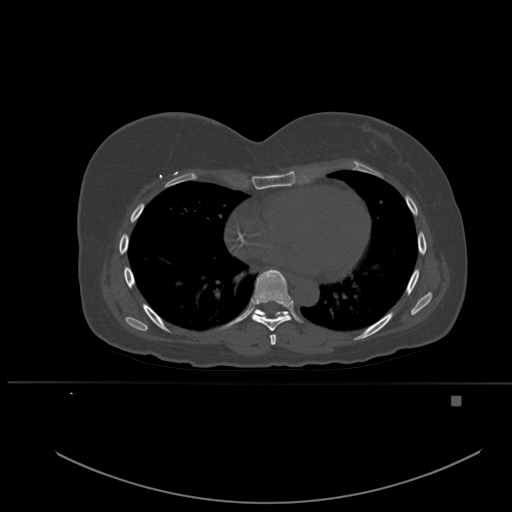
CT including the spine, one axial slice; position 332 of 651 along the scan axis; bone window (W 1800 / L 400 HU); 1.5 mm slice thickness; 512 × 512 image matrix, field of view 443 × 443 mm. Female patient, age 49 years. Case-level facts recorded for this patient, not image findings: primary cancer: breast; vertebrae with lytic lesions (as recorded): L3, T12, L4.
Annotated regions visible in this slice (semi-automatically segmented with operator editing):
- T6 vertebra: box from (x=270, y=334) to (x=277, y=345) px
- T7 vertebra: (x=251, y=269)–(x=294, y=331)
- T8 vertebra: (x=254, y=309)–(x=288, y=317)